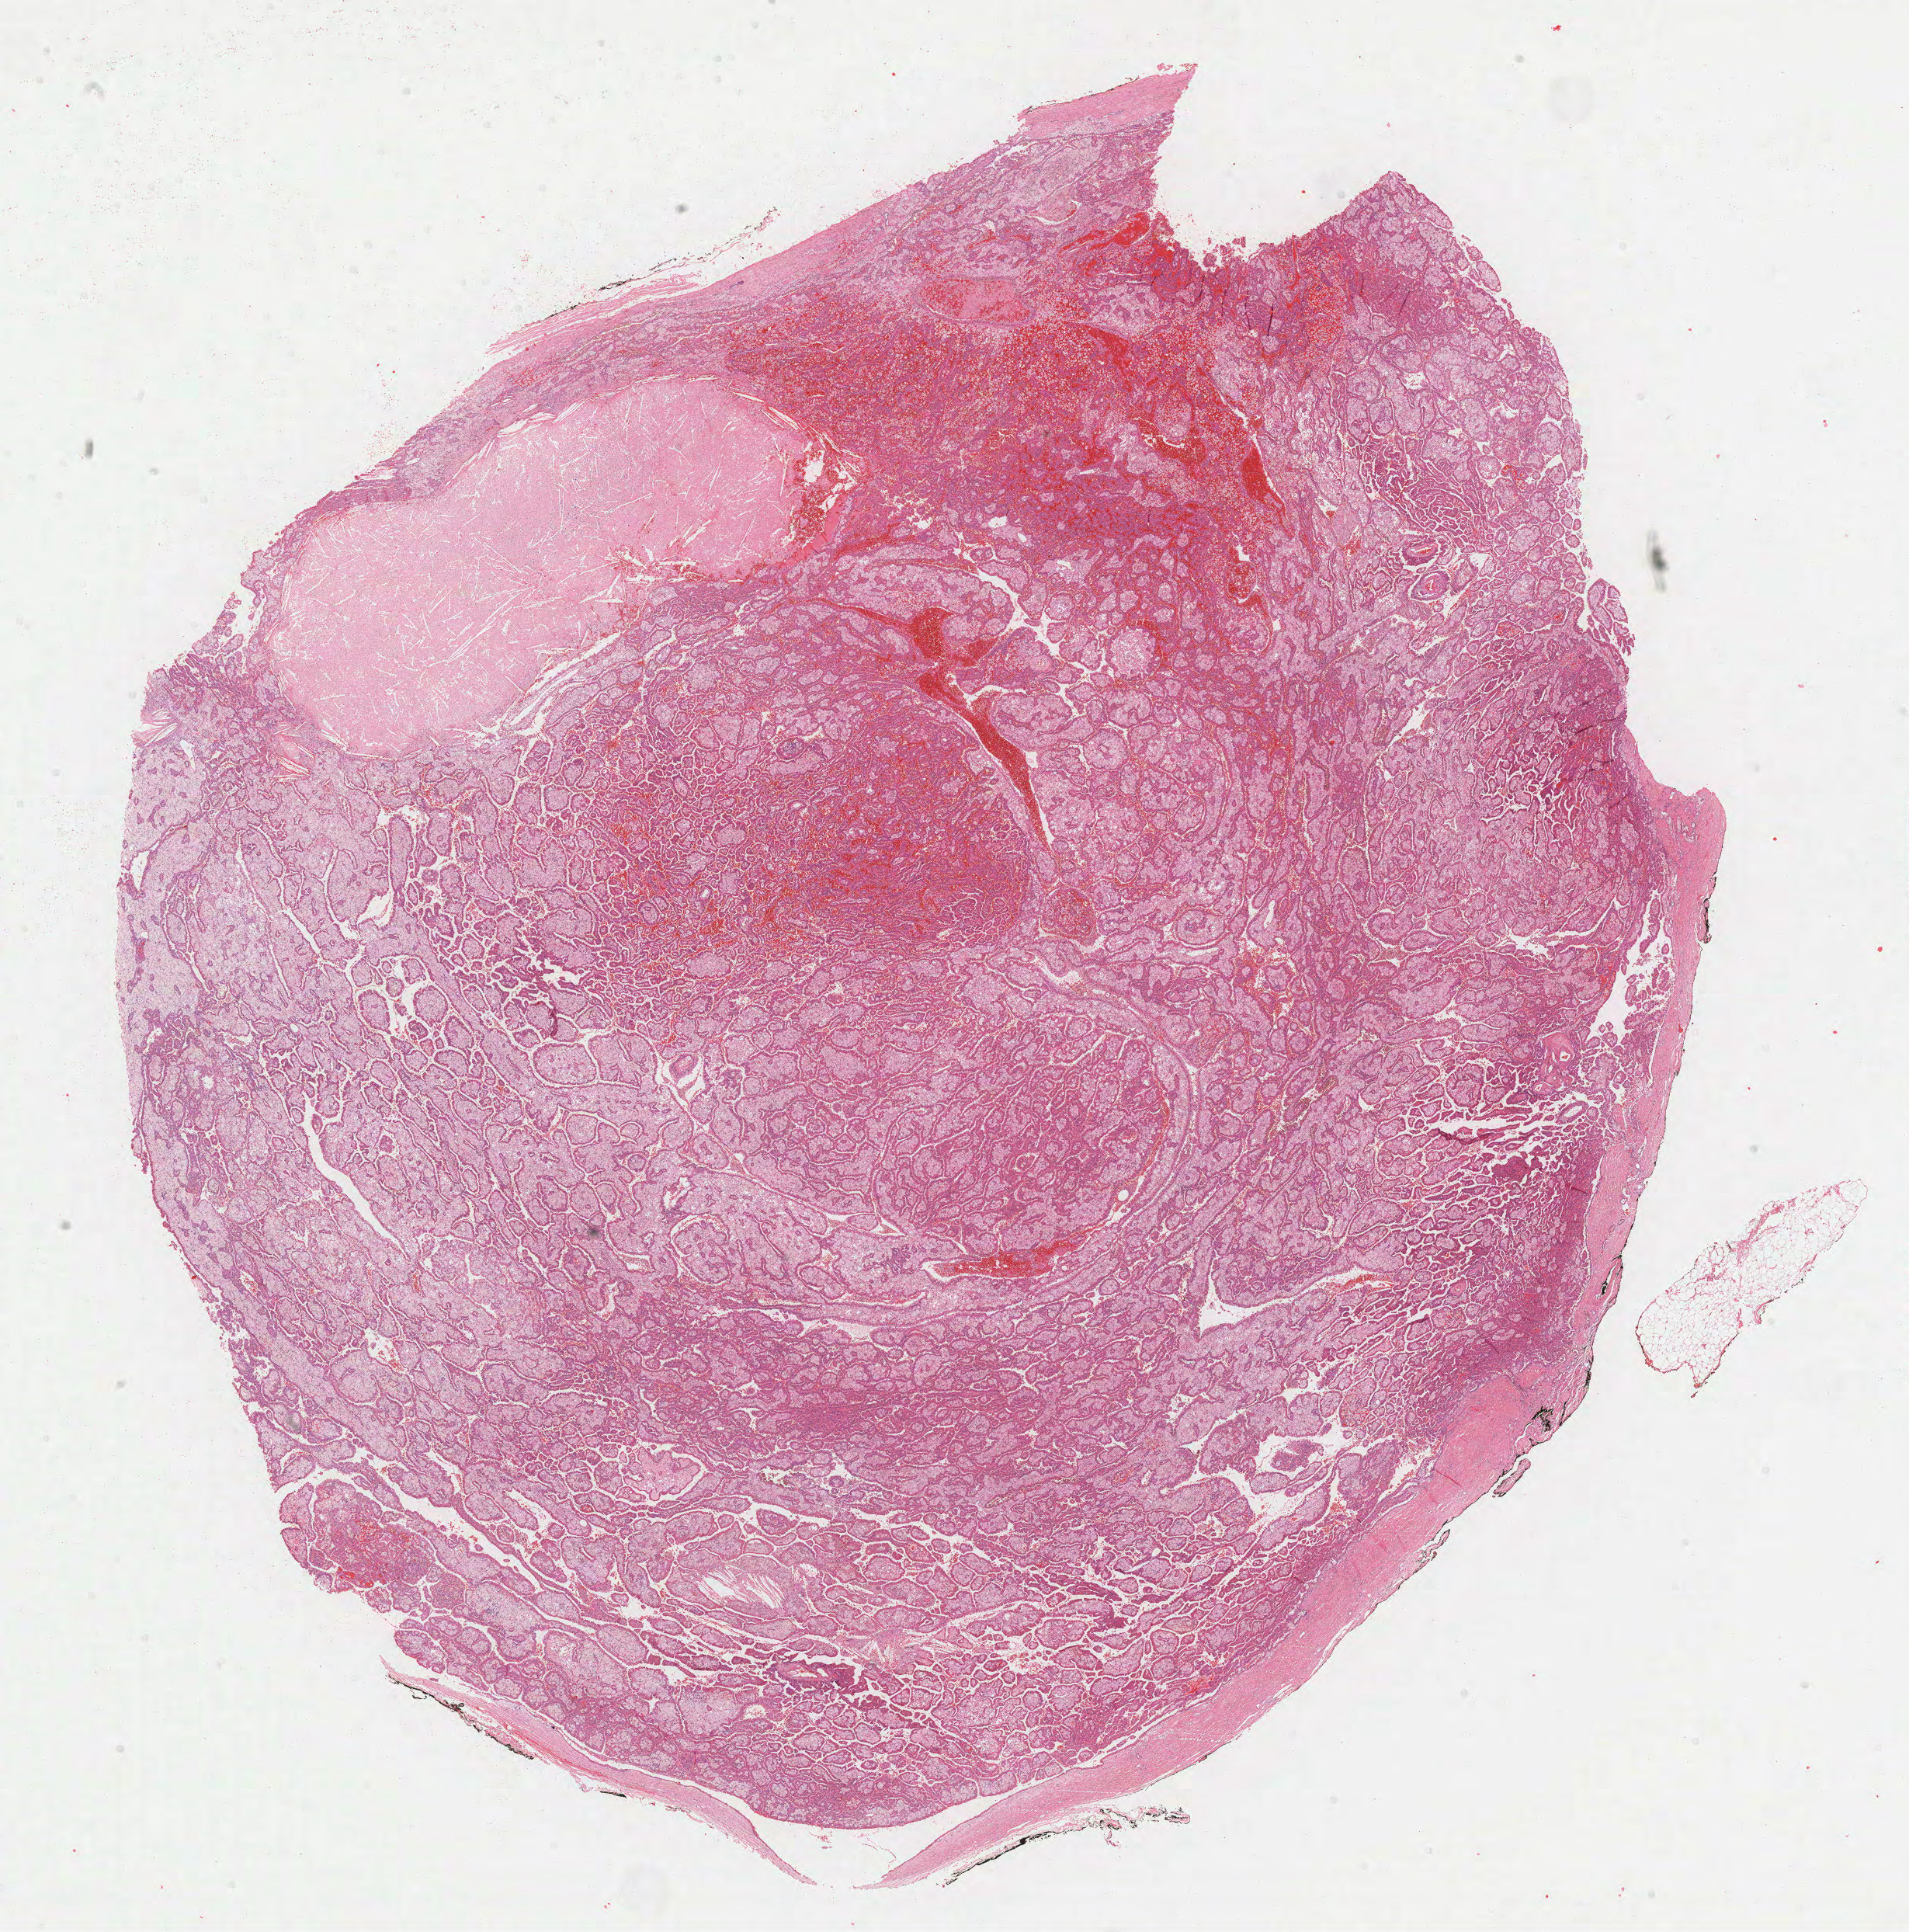
Hematoxylin and eosin (H&E) stained whole-slide image — low-resolution overview of the scanned area, about 19.9 x 20.1 mm. FFPE section. Primary tumour sample from the kidney. Patient: male, age at initial diagnosis 71 years.
AJCC pathologic stage: I (7th edition). Pathologic diagnosis: Papillary adenocarcinoma, NOS.